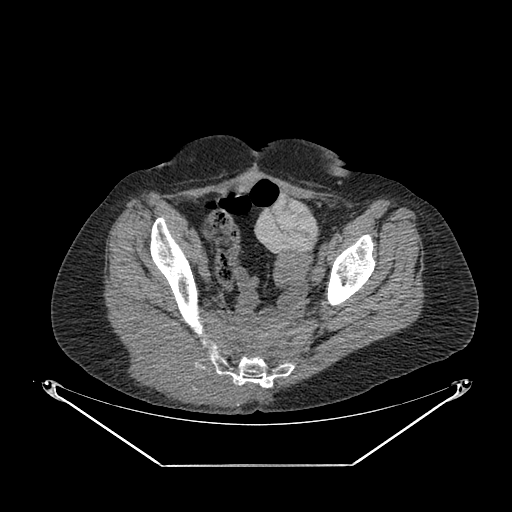
CT of an extremity soft-tissue mass (from a PET/CT study), one axial slice; slice 65 of 267 in the series (ordered by position); reconstruction kernel SOFT; soft-tissue window (W 400 / L 40 HU); 3.75 mm slice thickness; 512 × 512 image matrix, field of view 500 × 500 mm. Female patient. From the clinical record (not read from this slice): histological type: spindle cell suggestive of myxofibrosarcoma; grade: intermediate; site of the primary tumour: right buttock.
Outlined on this slice (expert contour drawn on MRI and transferred to this co-registered scan by the dataset authors):
- gross tumour volume (mass): box from (x=123, y=324) to (x=248, y=410) px